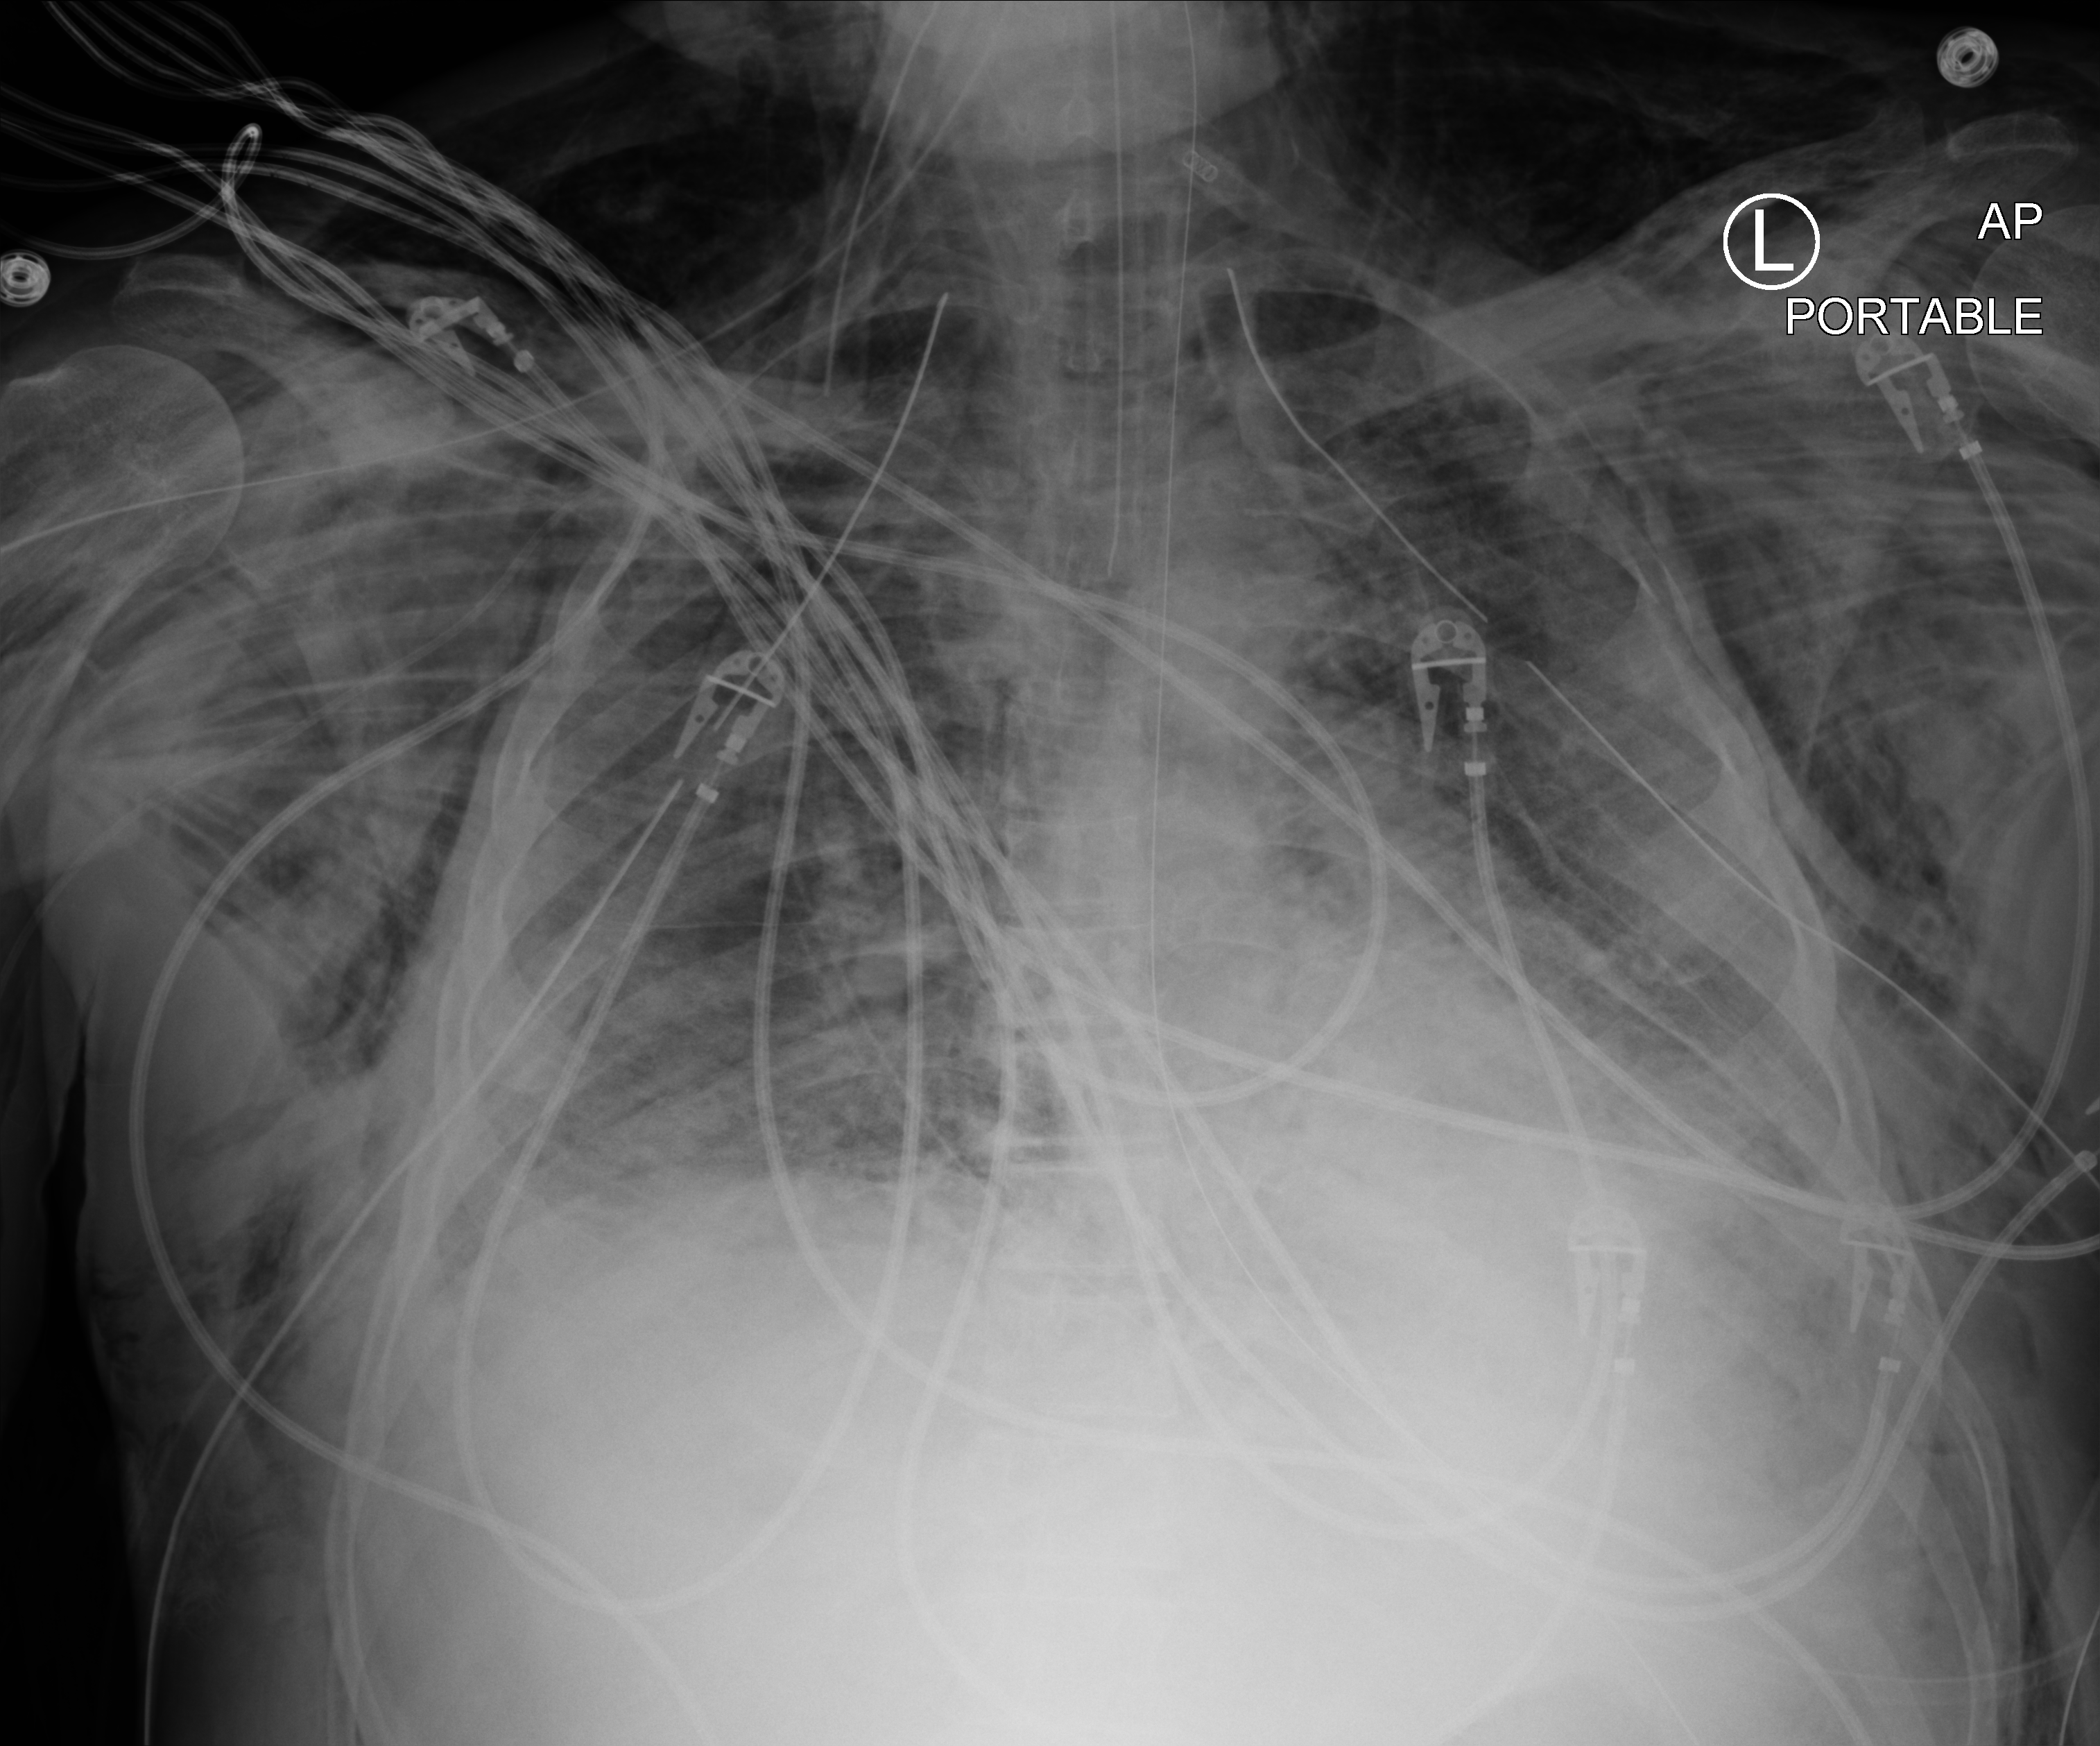
Bedside chest radiograph (computed radiography), anteroposterior (AP) projection. Male patient hospitalised with COVID-19, age 18–59 years.
From the hospital-stay record, not from the radiograph (when in the stay this image was taken is not recorded): hypertension (admission record): yes; diabetes (admission record): no.